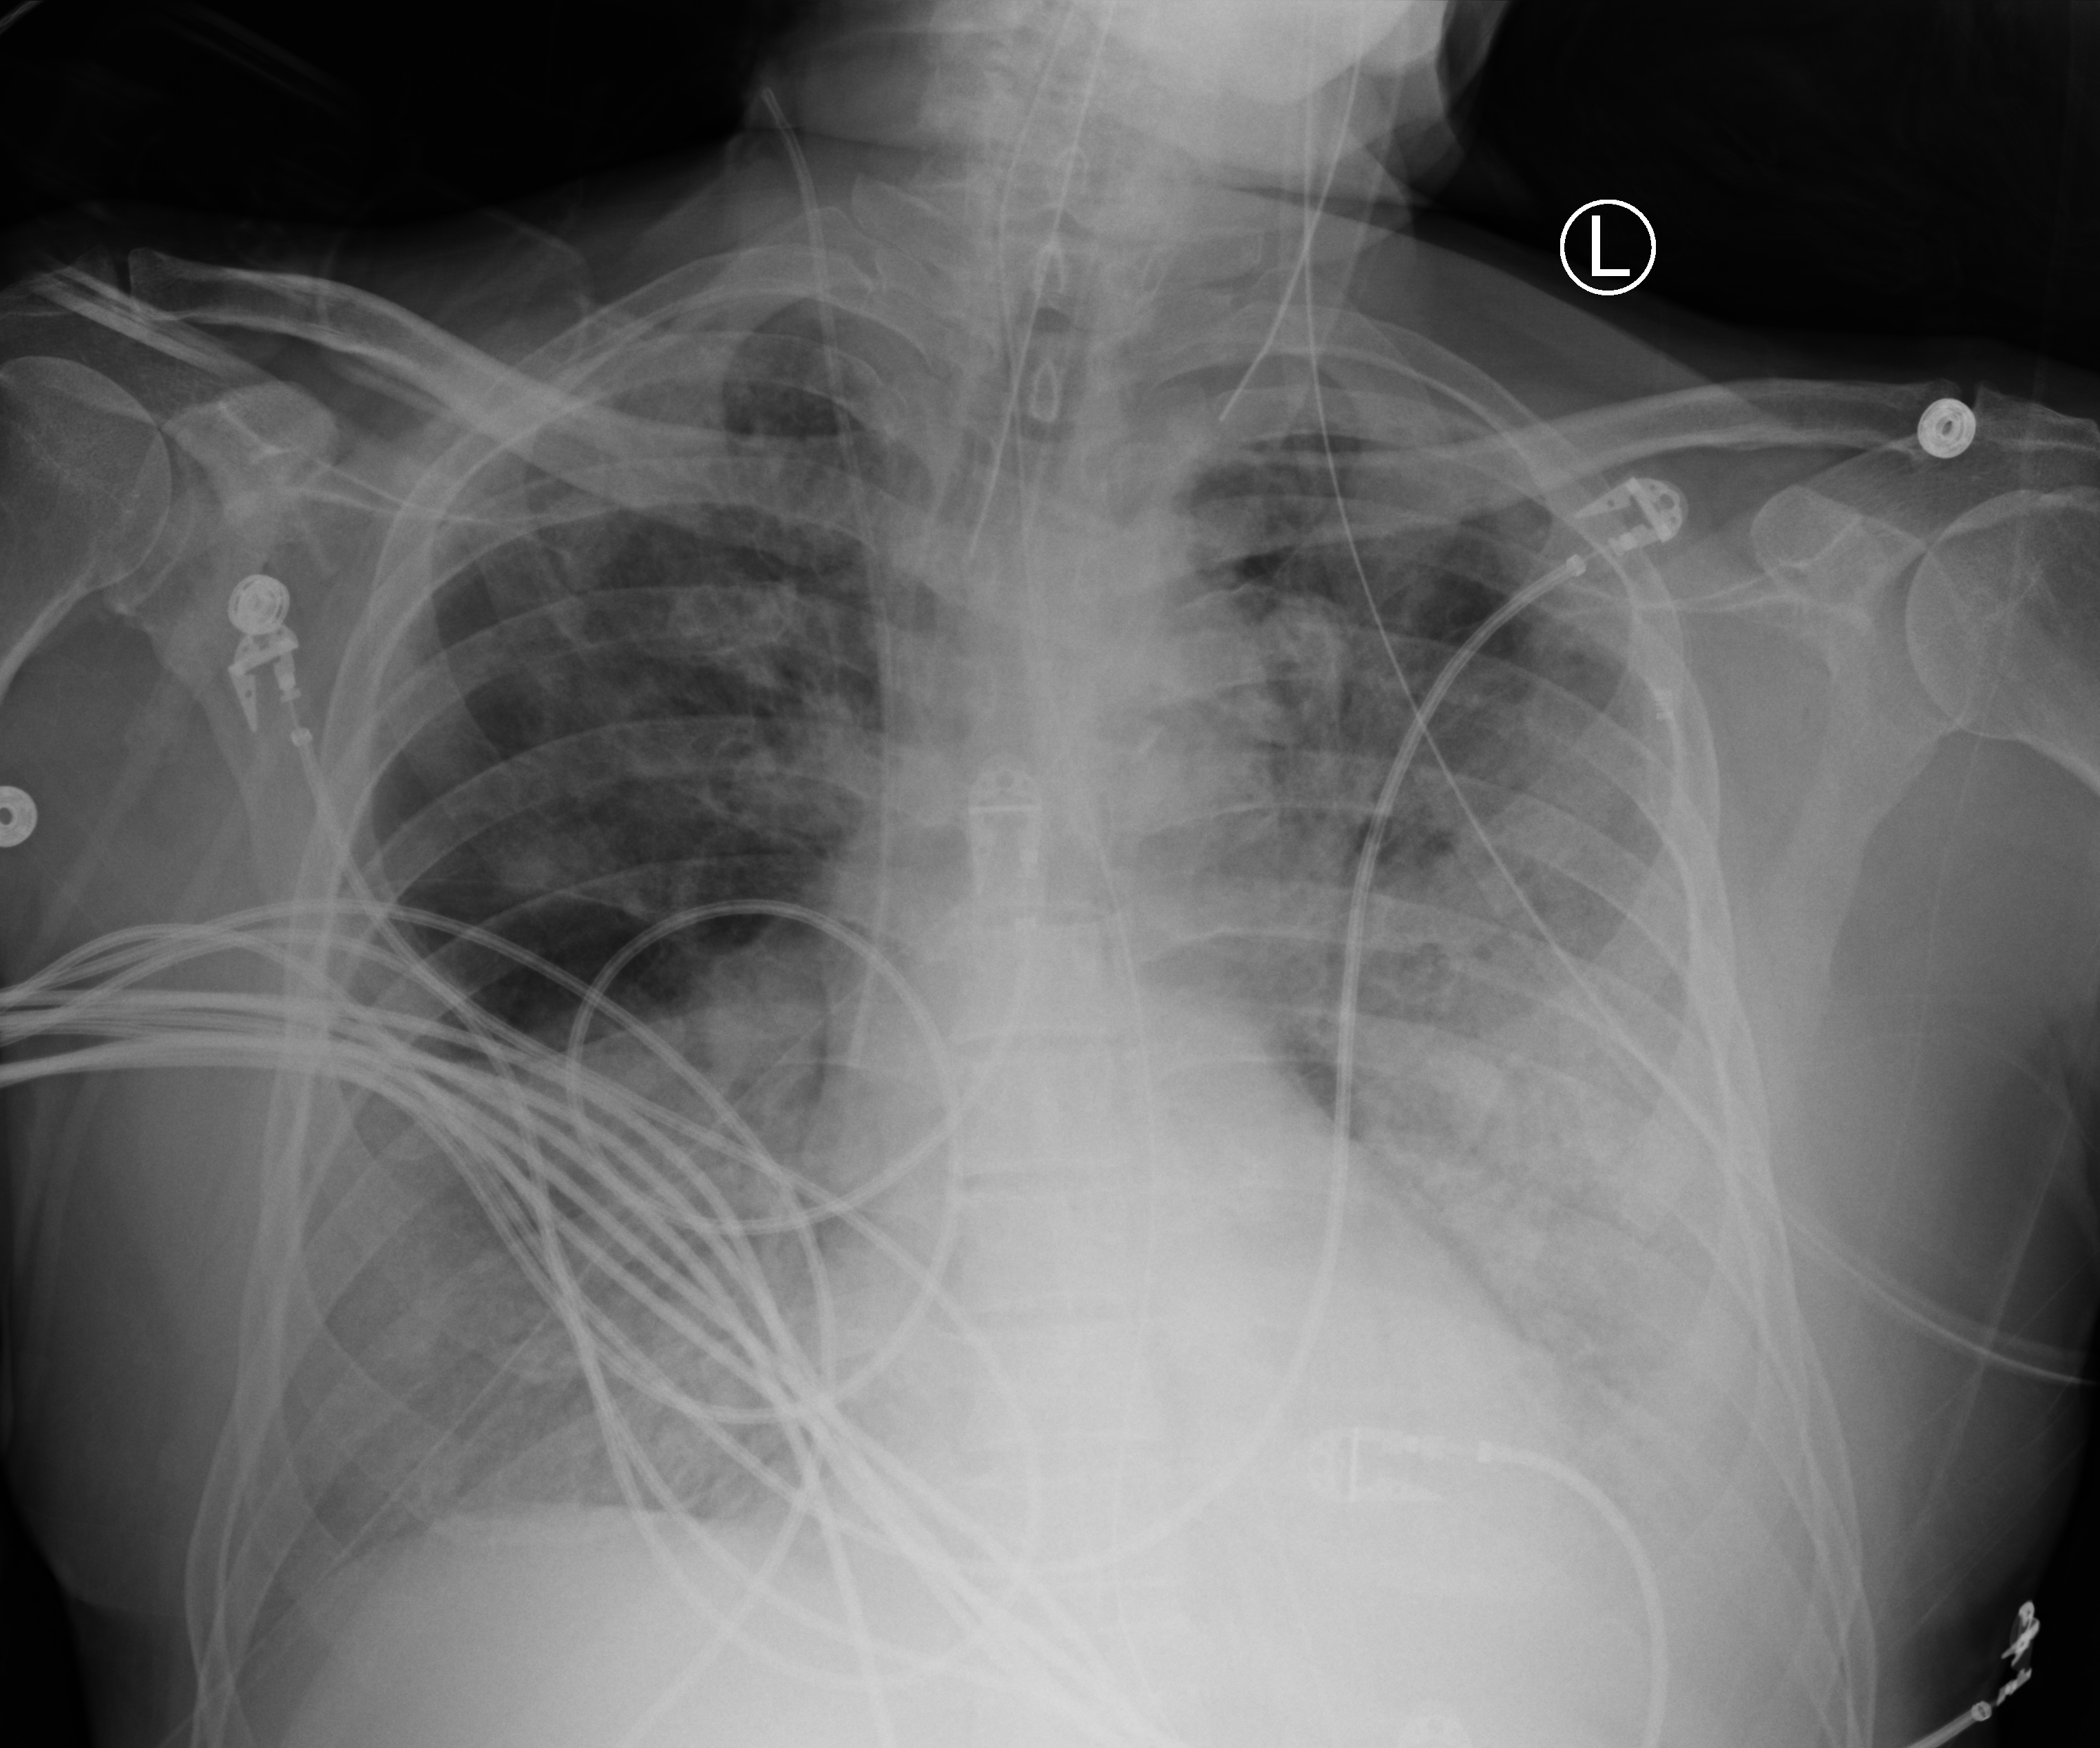
Chest X-ray (portable), anteroposterior (AP) projection. Male patient hospitalised with COVID-19, age 60–74 years.
From the hospital-stay record, not from the radiograph (when in the stay this image was taken is not recorded):
- diabetes (admission record): no
- mechanically ventilated during this hospital stay: yes
- length of hospital stay: 31 days